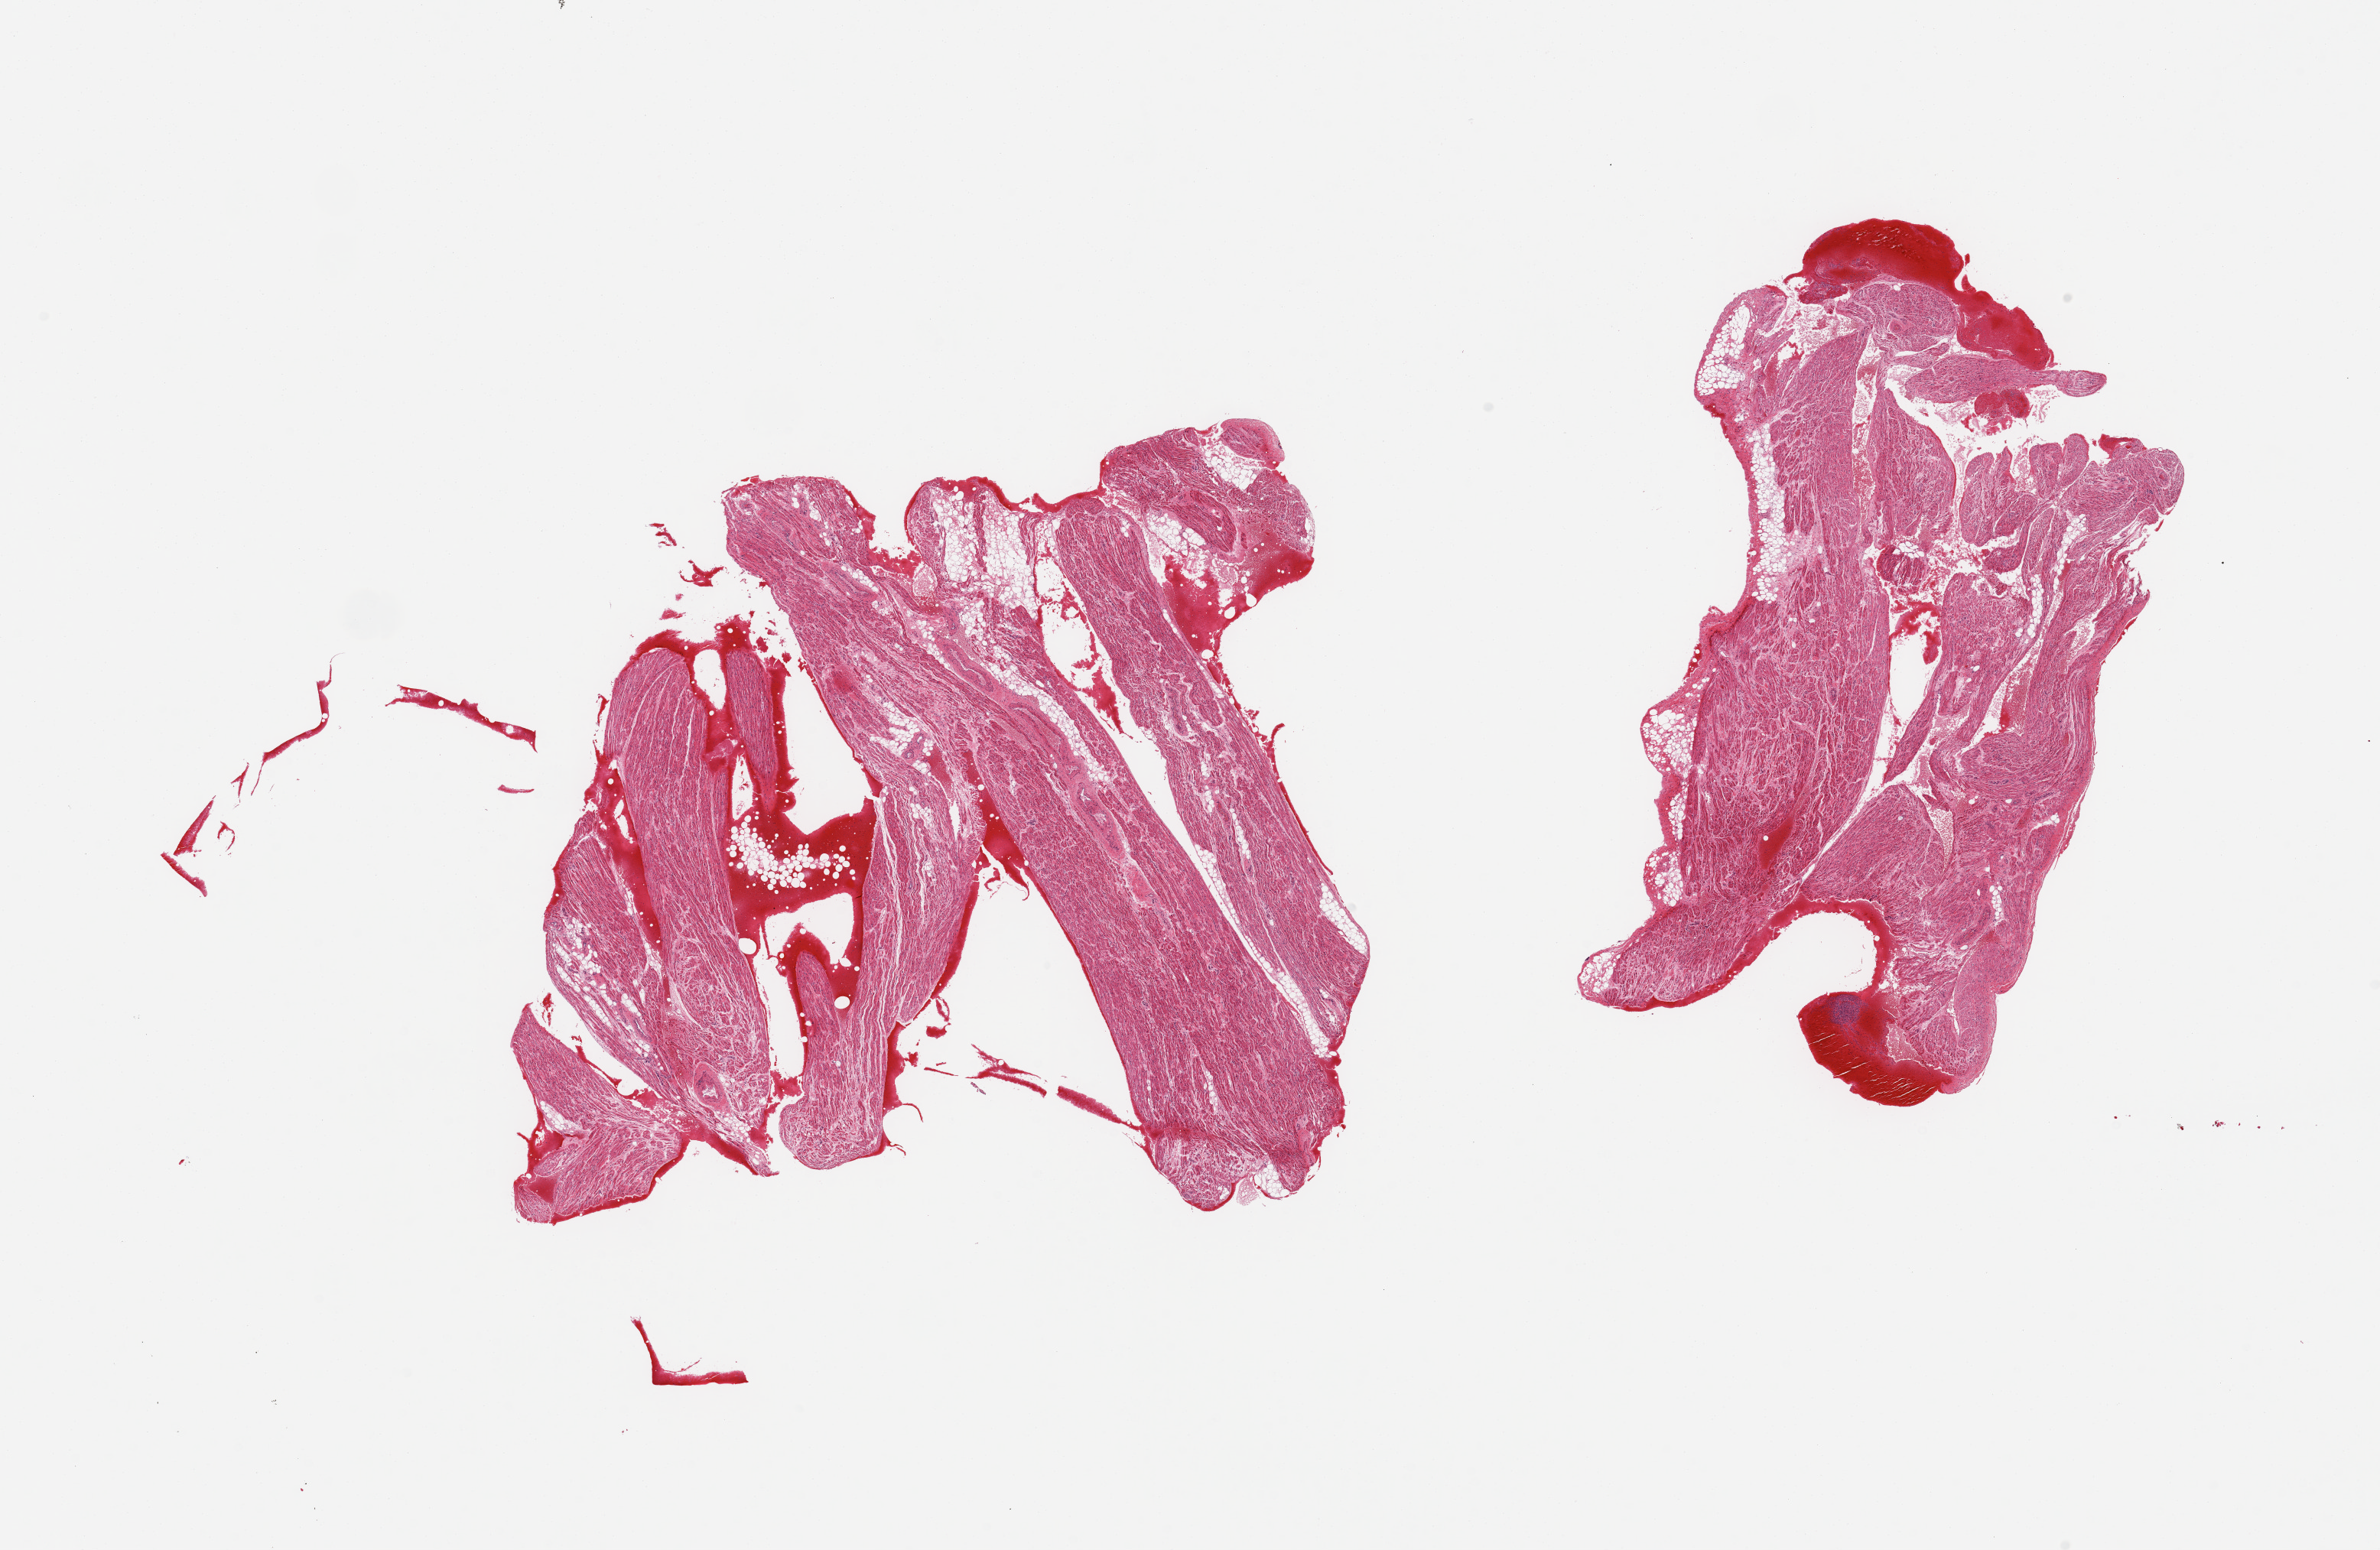
Whole-slide image, hematoxylin and eosin (H&E) stain, low-resolution overview of the scanned area, about 24.6 x 16.0 mm (from a 20x scan); PAXgene-fixed paraffin-embedded (PFPE) section; target tissue: auricular appendage; donor tissue sample. Female donor.
Pathologist's review note for this sample: 2 pieces, no abnormalities.